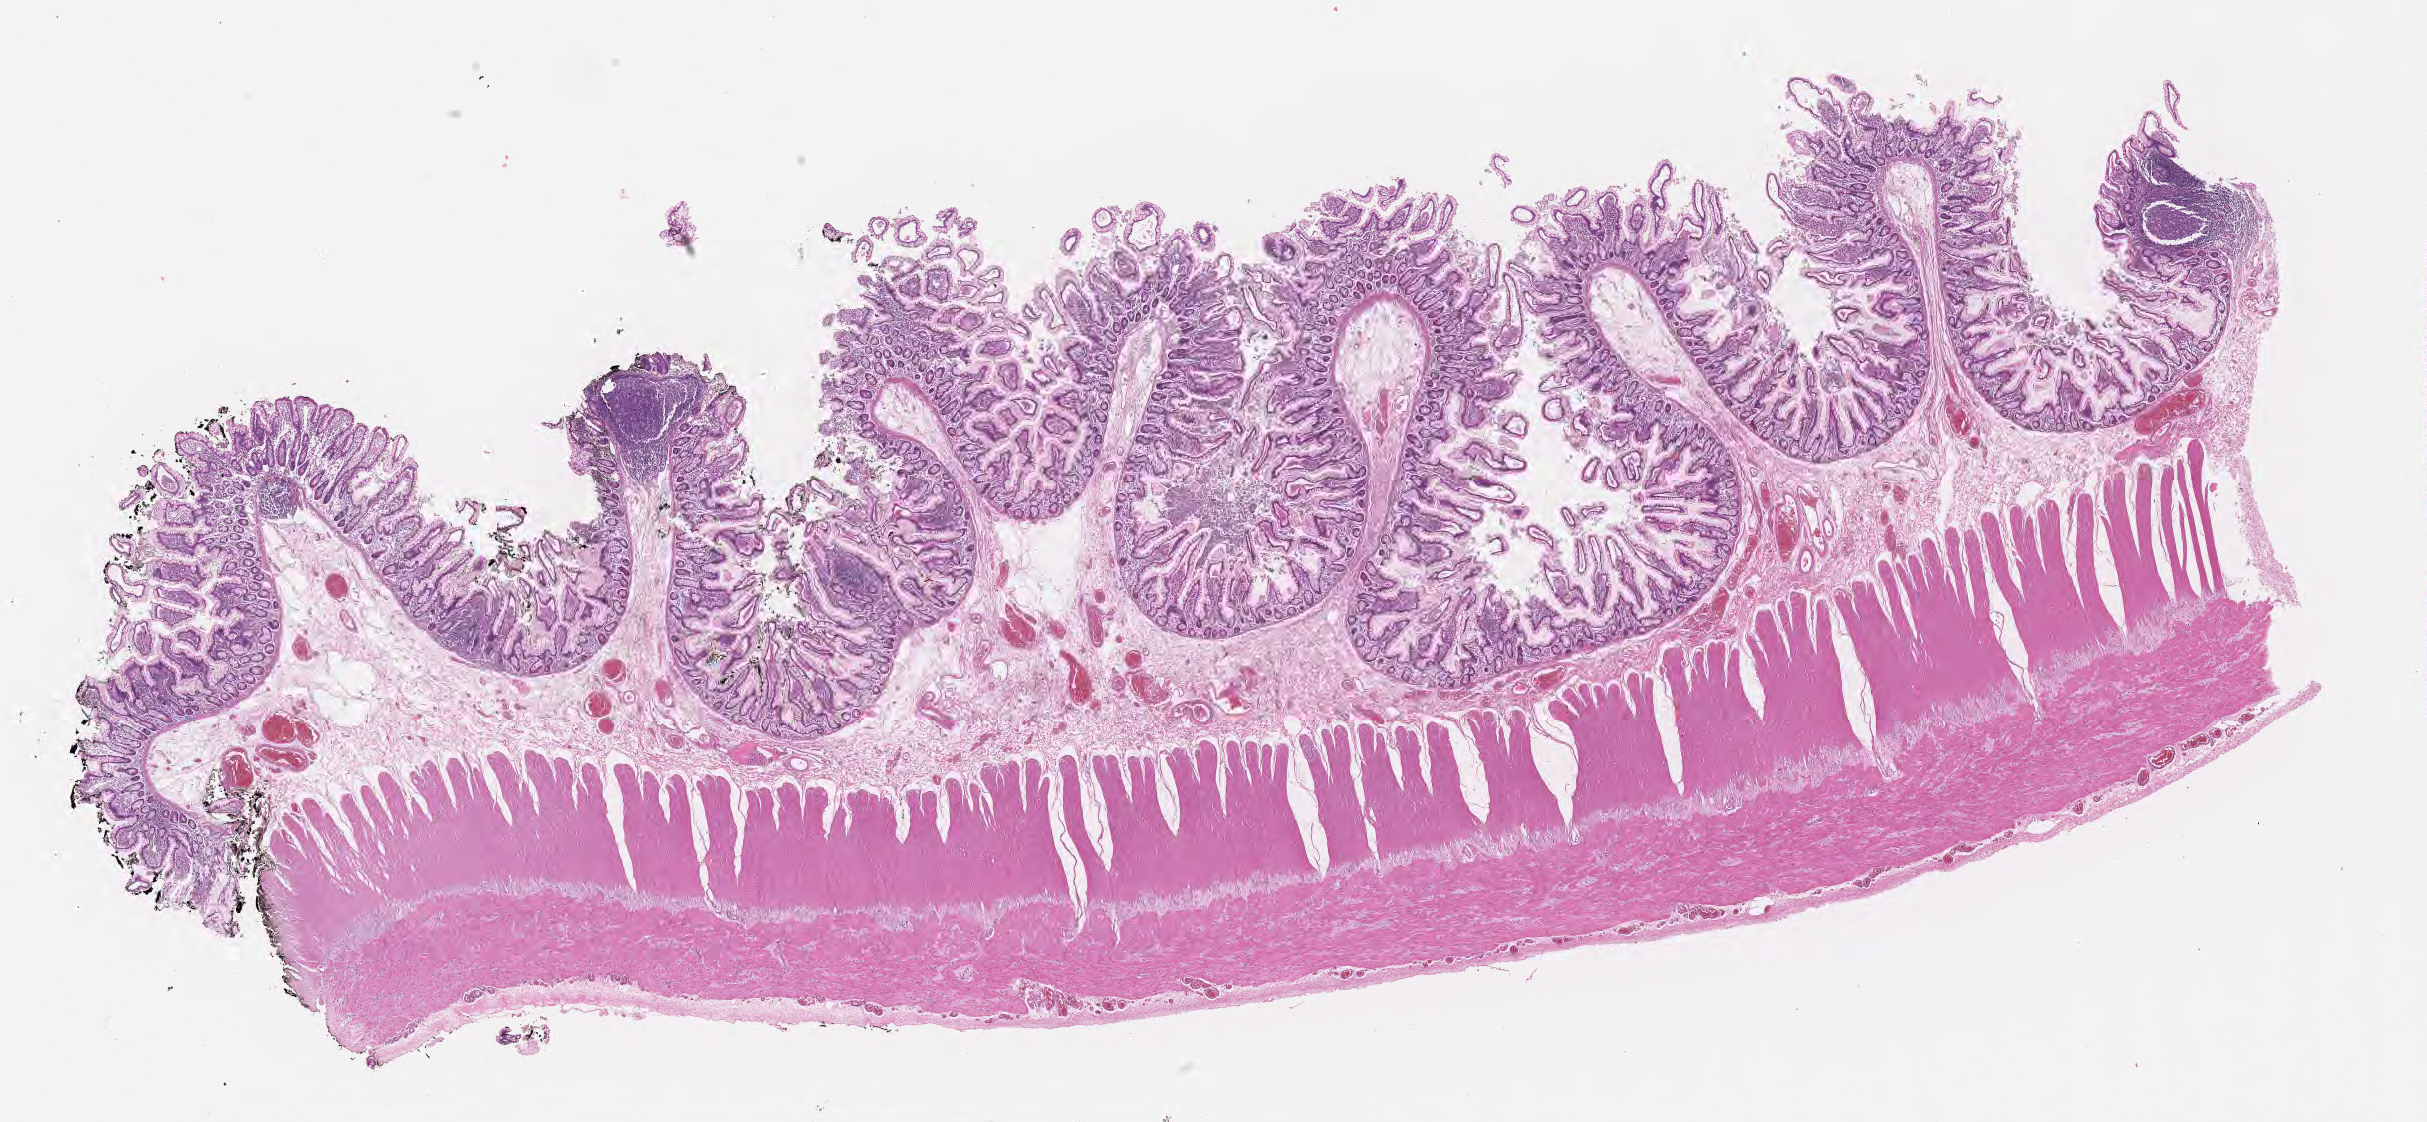
Haematoxylin and eosin whole-slide image, whole scanned area (about 19.6 x 9.1 mm) shown as a low-resolution overview. FFPE section. Specimen: non-tumor (normal tissue) sample from a patient with burkitt lymphoma, NOS. Patient: female, age at initial diagnosis 8 years. Composition of this section per pathologist review: tumor cells 0%, tumor nuclei 0%, stromal cells 0%, necrosis 0%, normal cells 100%. Inflammatory infiltration, as recorded: lymphocyte infiltration 80%, monocyte infiltration 10%, neutrophil infiltration 5%.
* this section: non-tumor tissue sample; the patient's diagnosis is given above